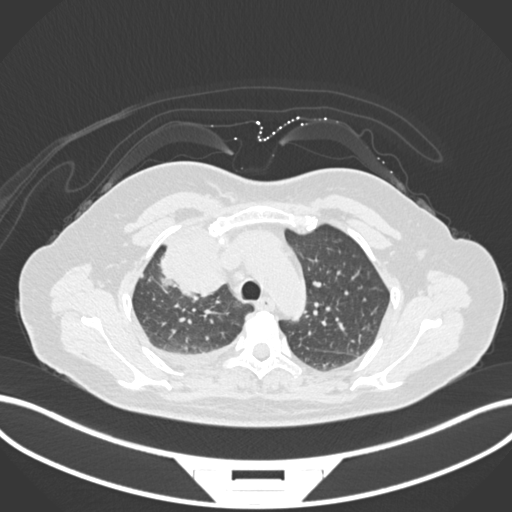
Chest CT, one axial slice. Slice 120 of 172 in the series (ordered by position). Reconstruction kernel B30f. 120 kVp. Lung window (W 1500 / L -600 HU). 512 × 512 image matrix, field of view 400 × 400 mm. Patient: female, 52 years. From the clinical record (not read from this slice): clinical TNM (as recorded): T3 N1 M1.
Structures marked on this image (bounding box drawn by a radiologist):
- lung tumour (recorded histology: adenocarcinoma): bounding box <153,218,230,297> (left, top, right, bottom; pixels)